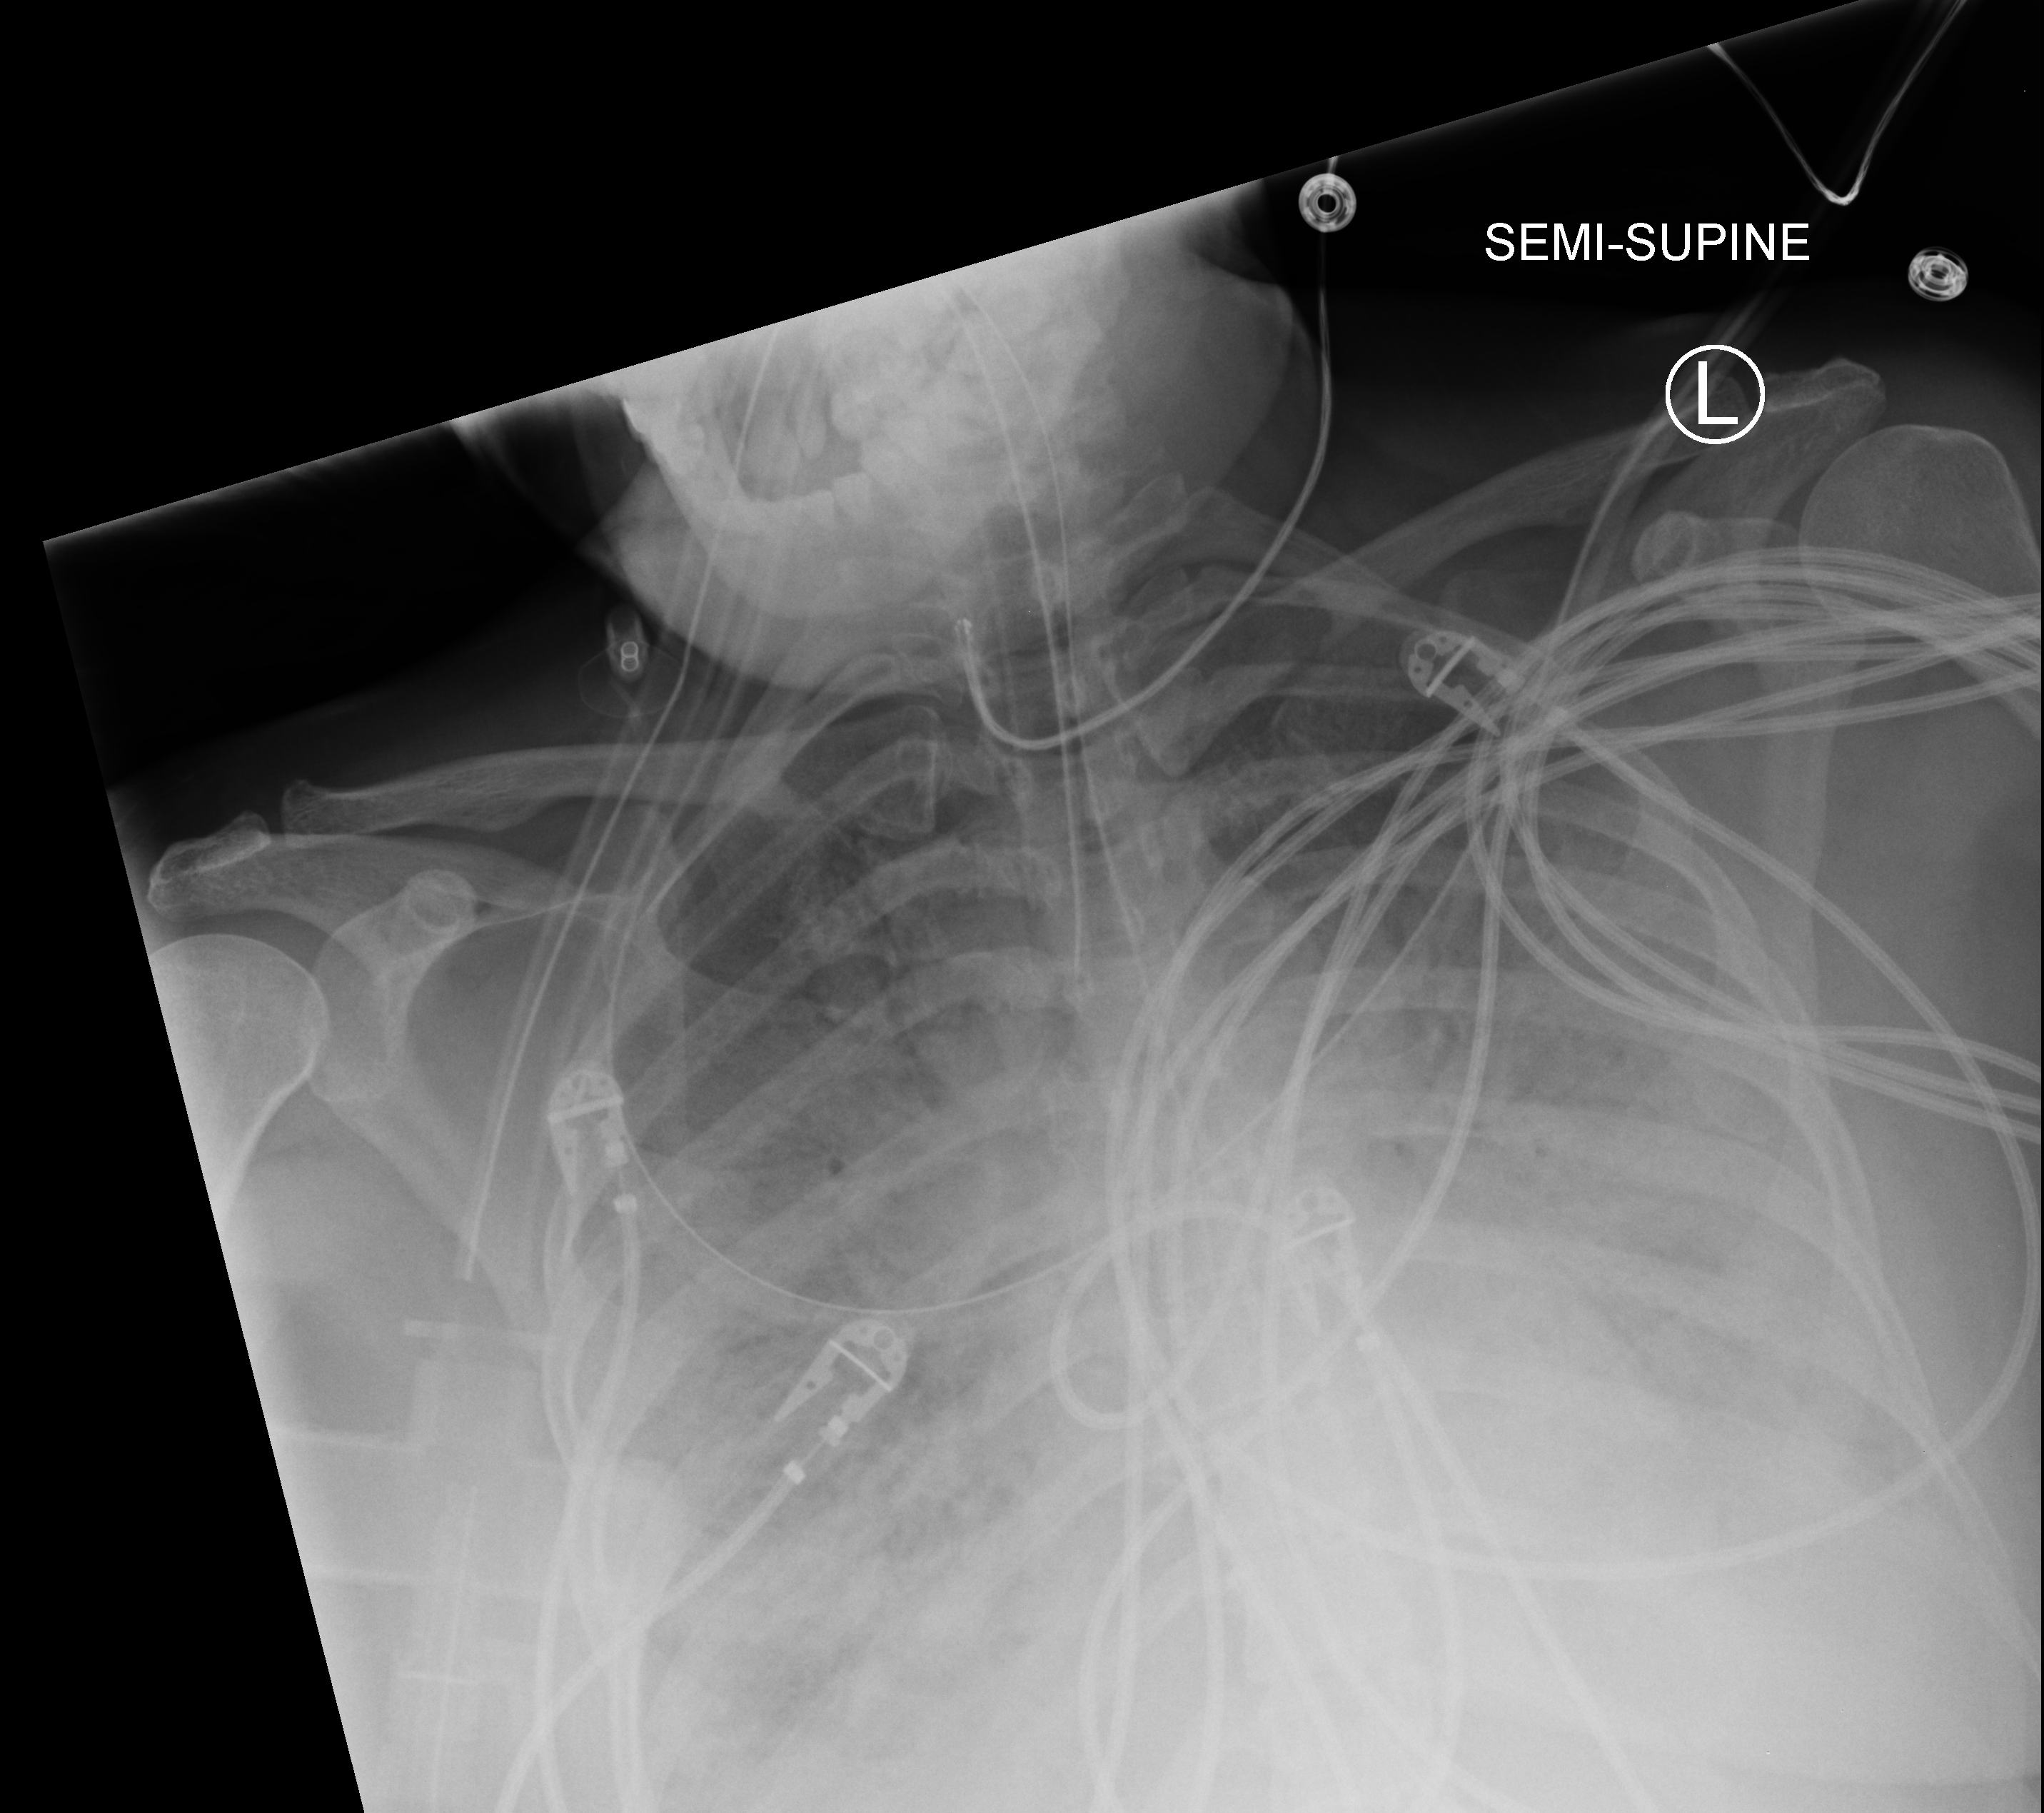
Chest X-ray (portable). Male patient hospitalised with COVID-19, age 18–59 years.
From the hospital-stay record, not from the radiograph (when in the stay this image was taken is not recorded): chronic kidney disease (admission record): no; length of hospital stay: 38 days; hypertension (admission record): yes.